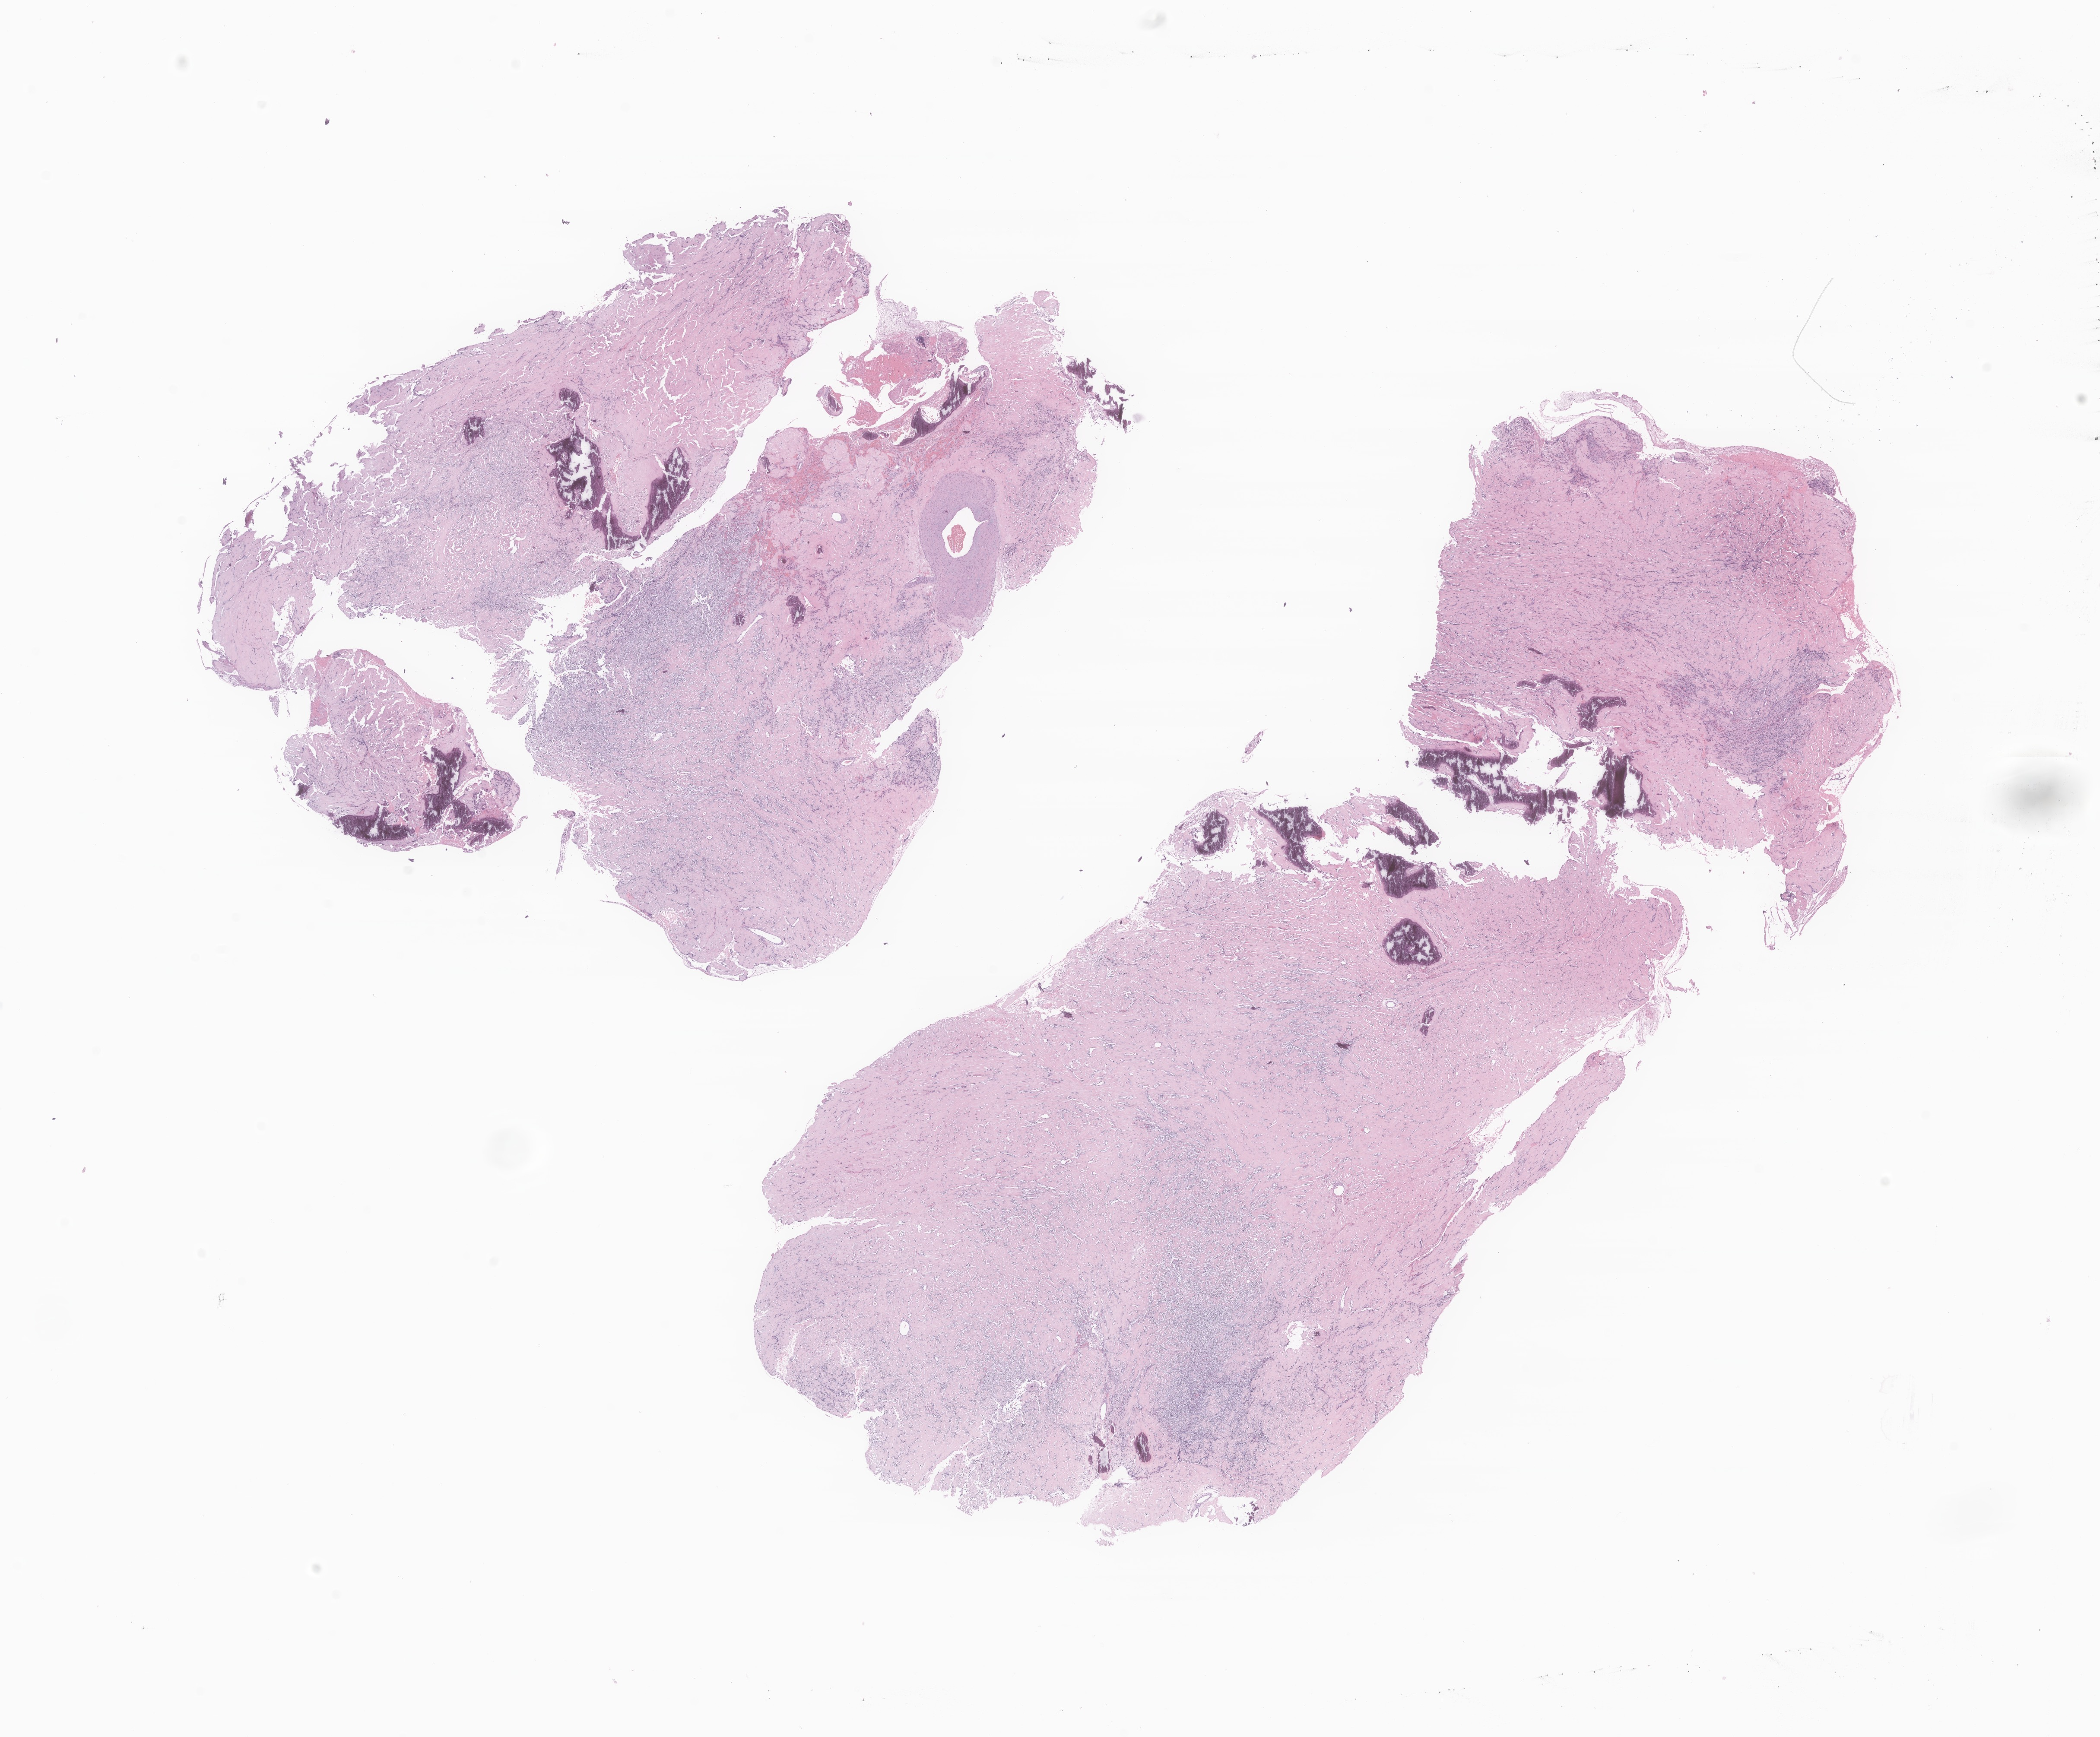
Whole-slide image, haematoxylin and eosin stain of tumor tissue from the respiratory and/or intrathoracic structure, low-resolution overview of the scanned area, about 20.5 x 17.0 mm. FFPE section. Patient: female, age 182 months (15 years 2 months).
- diagnosis: Neoplasm, malignant
- tissue or organ of origin (case record): overlapping lesion of respiratory system and intrathoracic organs